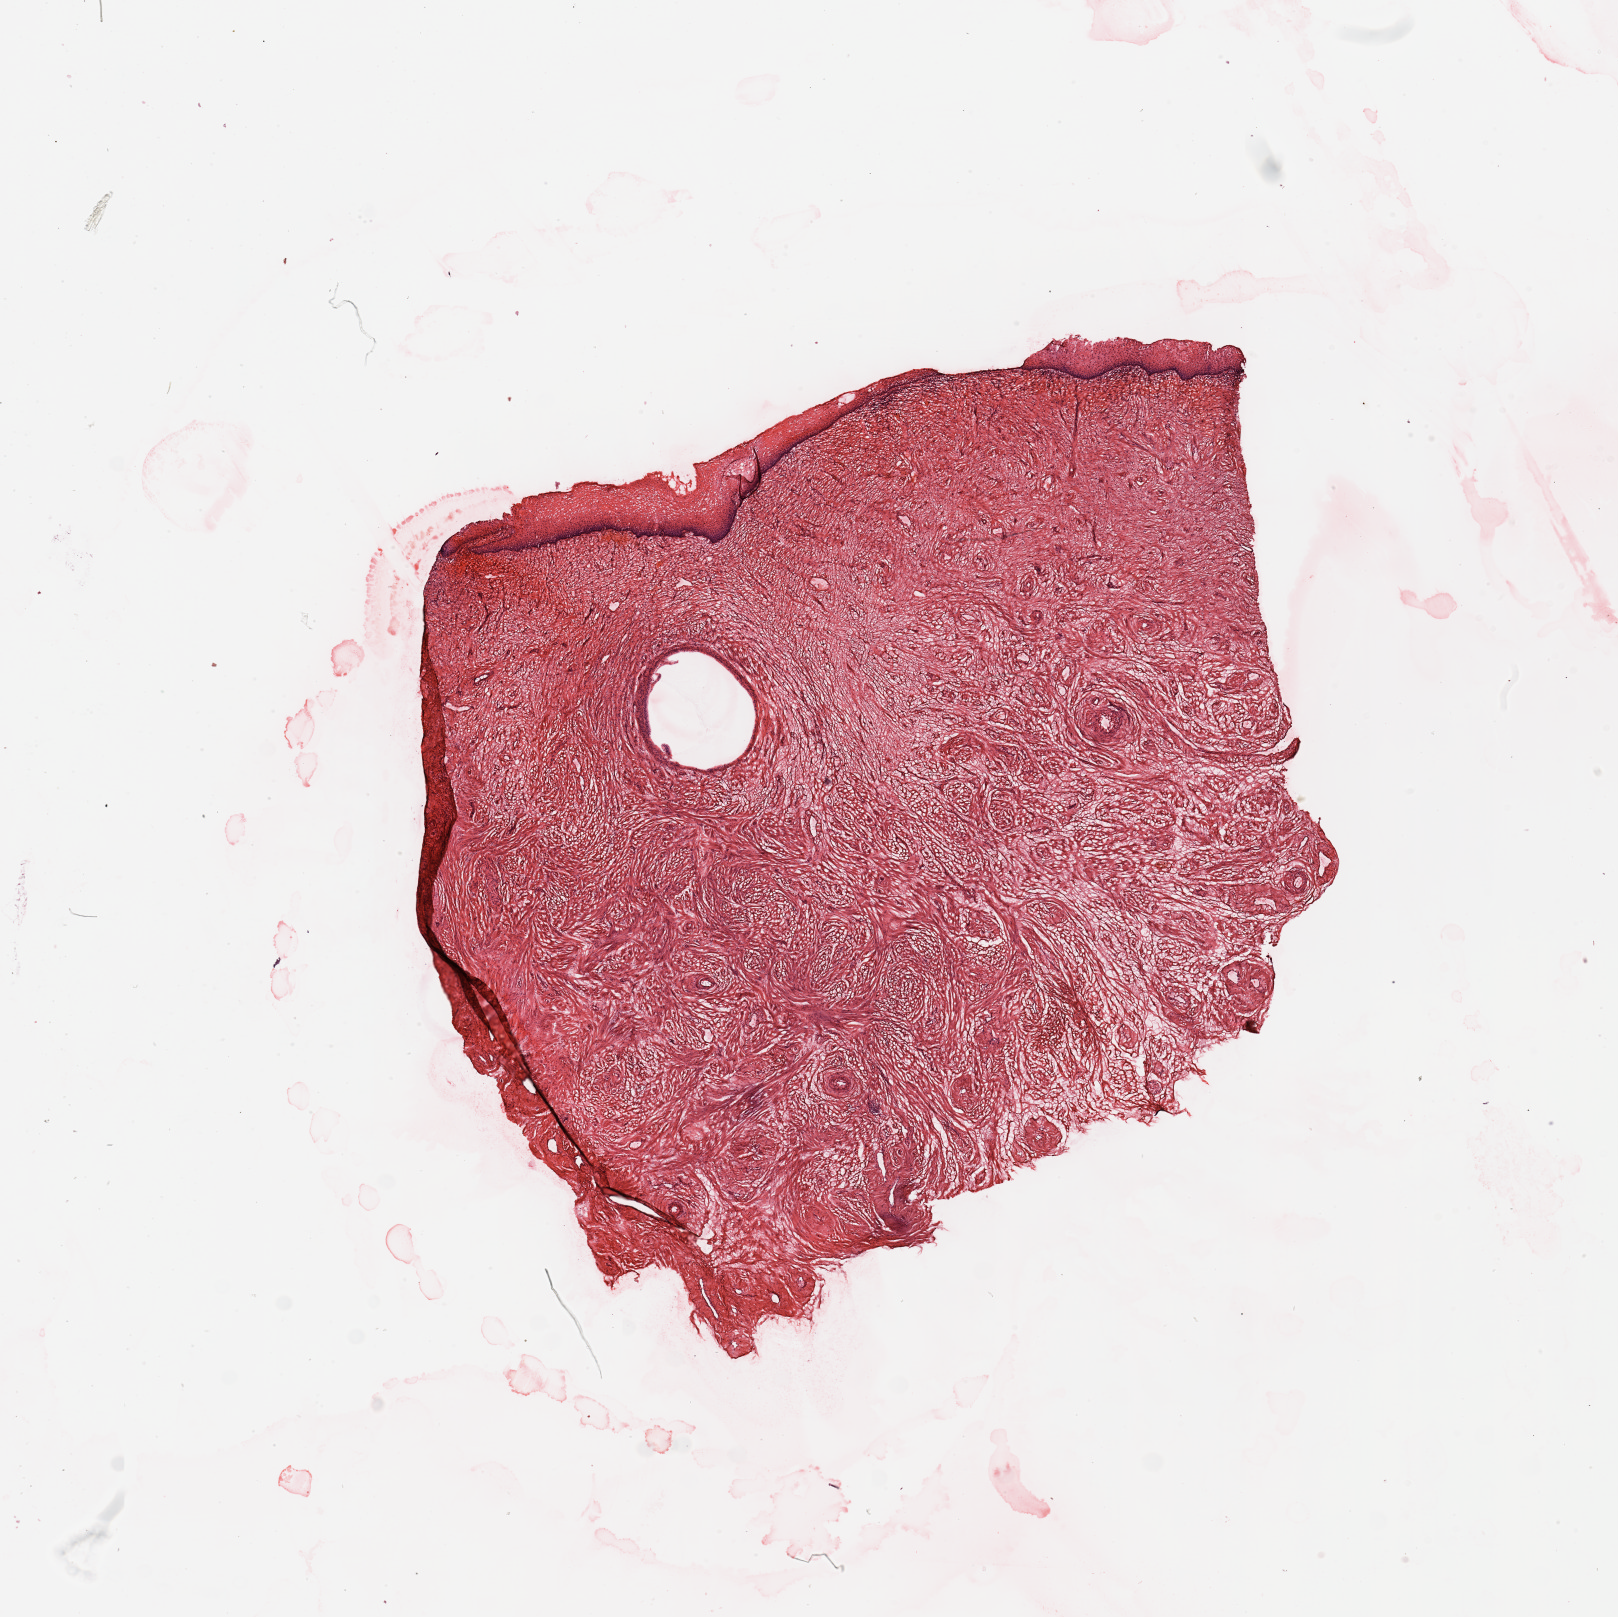
H&E-stained whole-slide image — whole scanned area (about 12.8 x 12.8 mm, acquisition: 20x scan) shown as a low-resolution overview; normal (non-tumour) tissue sample, uterus. Patient: female, age 65 years.
This section: normal (non-tumour) tissue from the same patient. Patient diagnosis: Endometrioid adenocarcinoma, NOS.